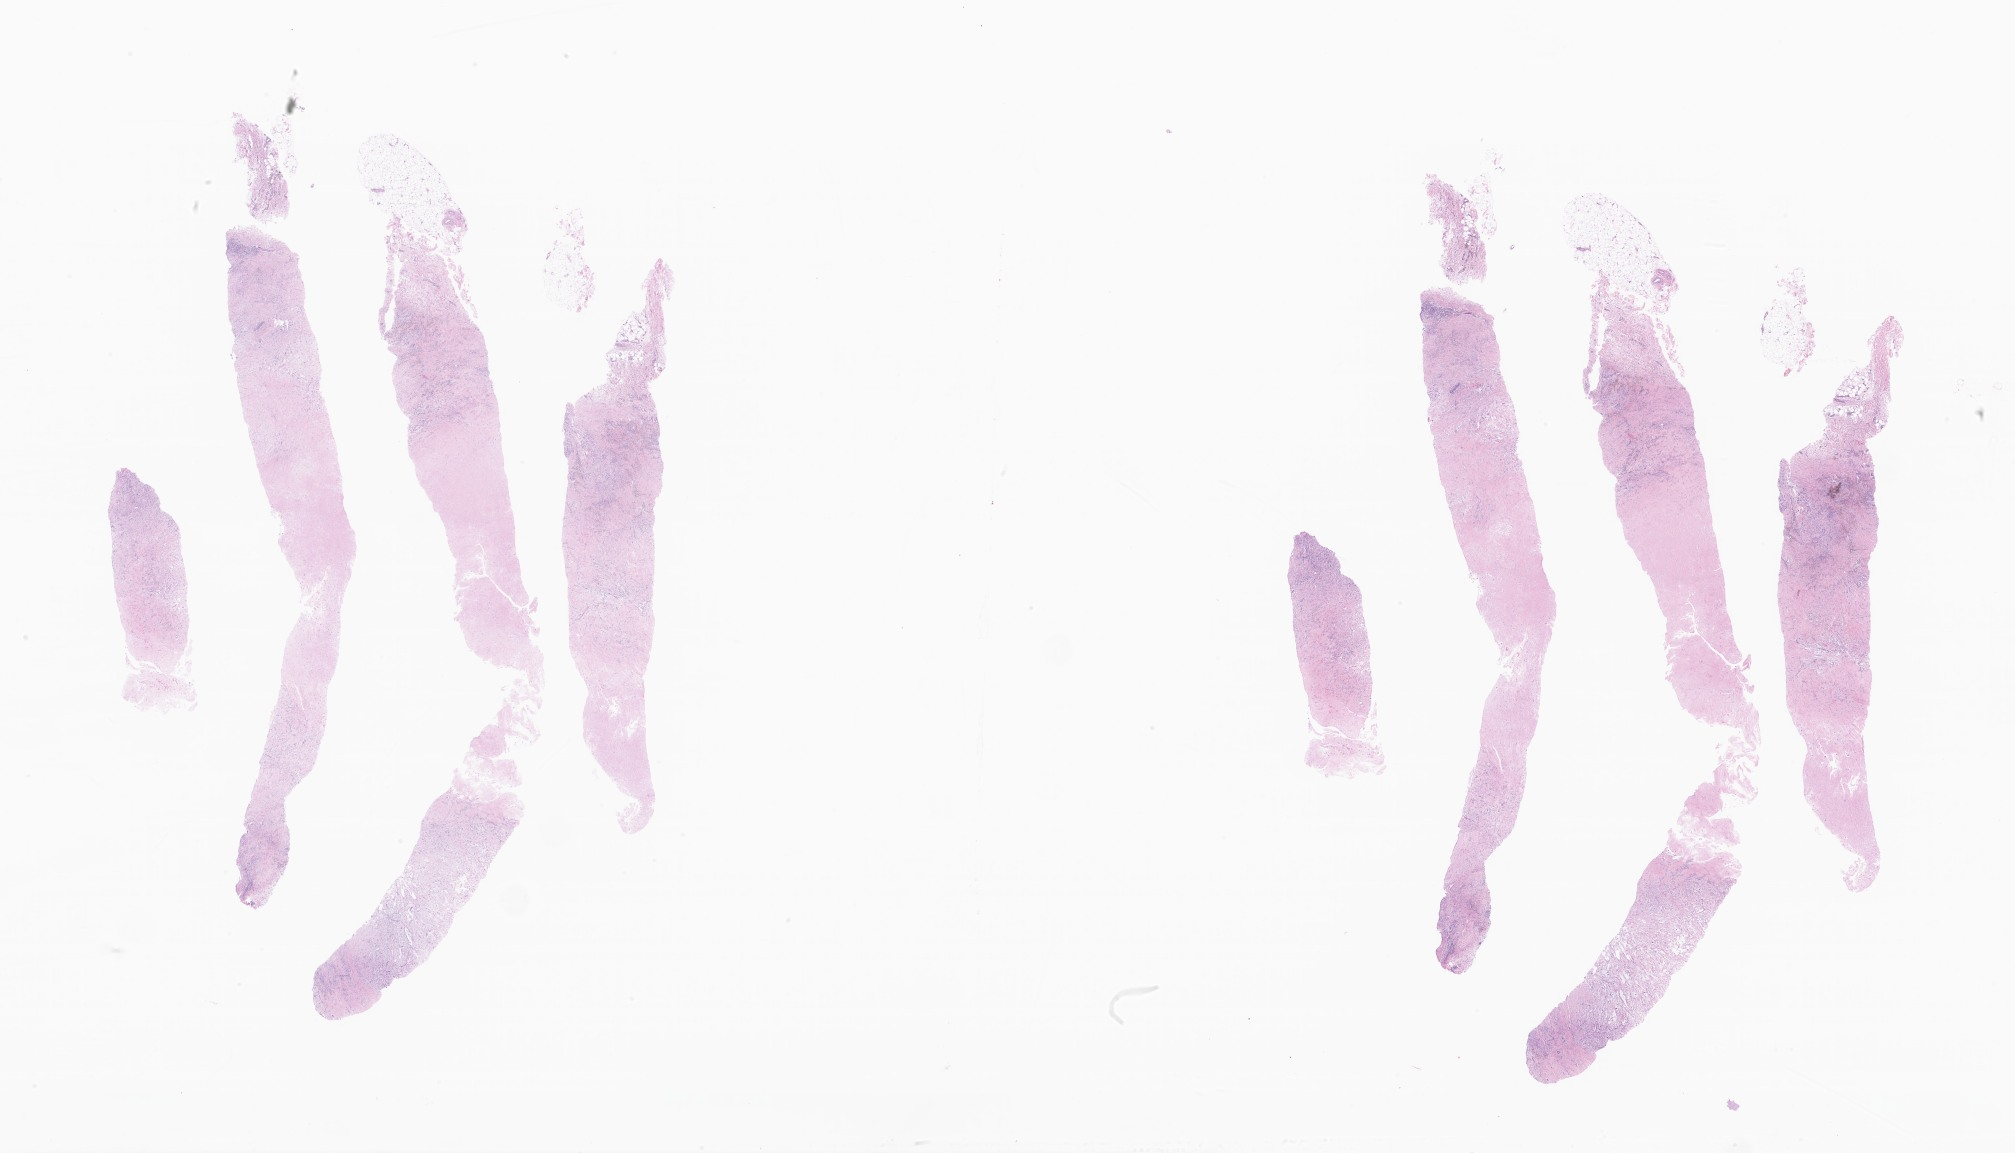
H&E whole-slide image of tumor tissue from the soft tissue of thorax — a low-resolution overview of the entire scanned area, about 34.0 x 19.4 mm, formalin-fixed, paraffin-embedded (FFPE) tissue. Patient male; age 196 months.
Diagnosis (ICD-O-3 morphology term): Aggressive fibromatosis.